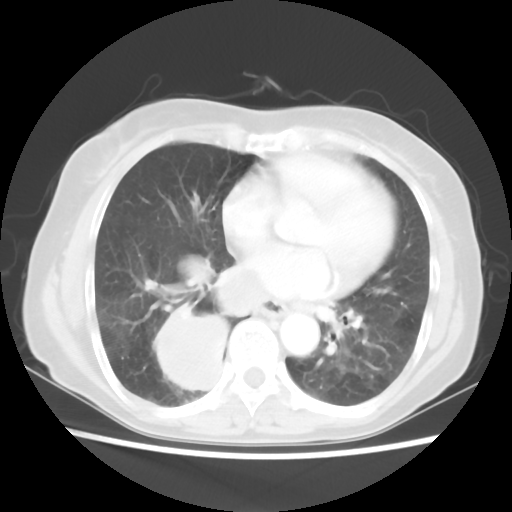
Chest CT, one axial slice; slice 26 of 56 in the series (ordered by position); reconstruction kernel STANDARD; lung window (W 1500 / L -600 HU); 512 × 512 image matrix, field of view 332 × 332 mm. Female patient, age 66 years. Case-level facts recorded for this patient, not image findings: clinical TNM (as recorded): T2 N3 M0; histopathological grade: G3.
Outlined on this slice (rectangle marked by the reading radiologist):
- lung tumour (recorded histology: small cell carcinoma): bounding box [x1, y1, x2, y2] px = [147, 306, 237, 400]